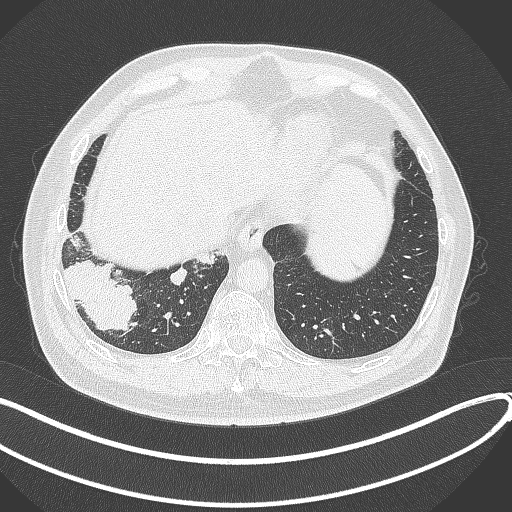
Chest CT, one axial slice; position 69 of 360 along the scan axis; reconstruction kernel B70f; 120 kVp; lung window (W 1500 / L -600 HU); 1 mm slice thickness; 512 × 512 image matrix, field of view 400 × 400 mm. Male patient, age 59 years.
Outlined on this slice (bounding box drawn by a radiologist):
- lung tumour (recorded histology: adenocarcinoma): bounding box (x1, y1, x2, y2) in pixels: (61, 252, 138, 336)